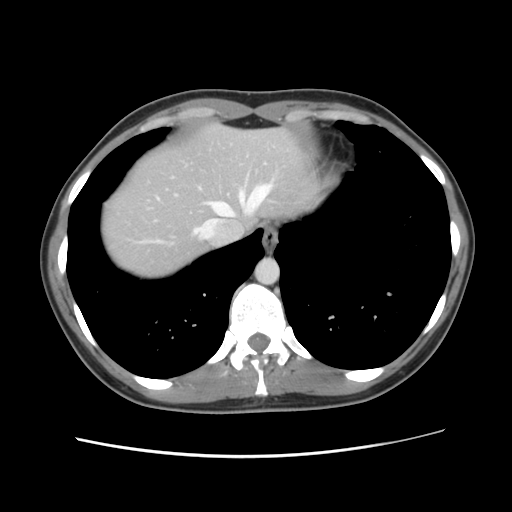
Contrast-enhanced abdominal CT, one axial slice. Position 107 of 134 along the scan axis. 120 kVp. Intravenous contrast given. Soft-tissue window (W 400 / L 40 HU). 2.5 mm slice thickness. 512 × 512 image matrix, field of view 339 × 339 mm. Female patient, age 33 years. From the clinical record (not read from this slice): diagnosis: colorectal cancer liver metastases, imaged before liver resection; multiple liver metastases: yes.
Structures marked on this image (outlined manually by an expert reader):
- hepatic veins: box from (x=156, y=183) to (x=274, y=242) px
- liver: (x=102, y=124)–(x=320, y=279)
- planned liver remnant (the part of the liver to remain after resection): (x=102, y=124)–(x=320, y=279)